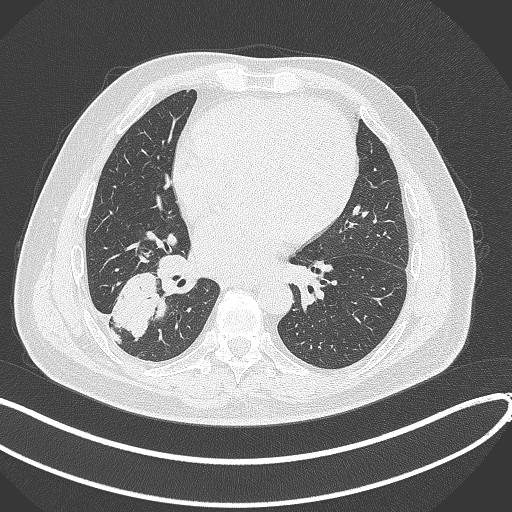
Chest CT, one axial slice; position 157 of 360 along the scan axis; reconstruction kernel B70f; 120 kVp; lung window (W 1500 / L -600 HU); 1 mm slice thickness; 512 × 512 image matrix. Patient: male, 59 years.
Annotated regions visible in this slice (rectangle marked by the reading radiologist):
- lung tumour (recorded histology: adenocarcinoma): bounding box (x1, y1, x2, y2) in pixels: (114, 266, 167, 341)